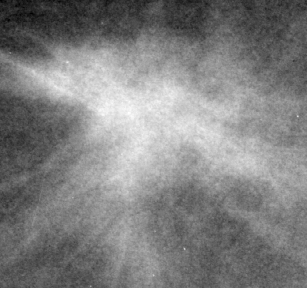
Crop from a digitized film mammogram around one marked abnormality; right breast; CC view; BI-RADS breast density category 1 (scale 1–4).
Finding: mass, shape irregular / architectural distortion, margins spiculated; BI-RADS assessment category 5; pathology result (as recorded, not read from the image): malignant.